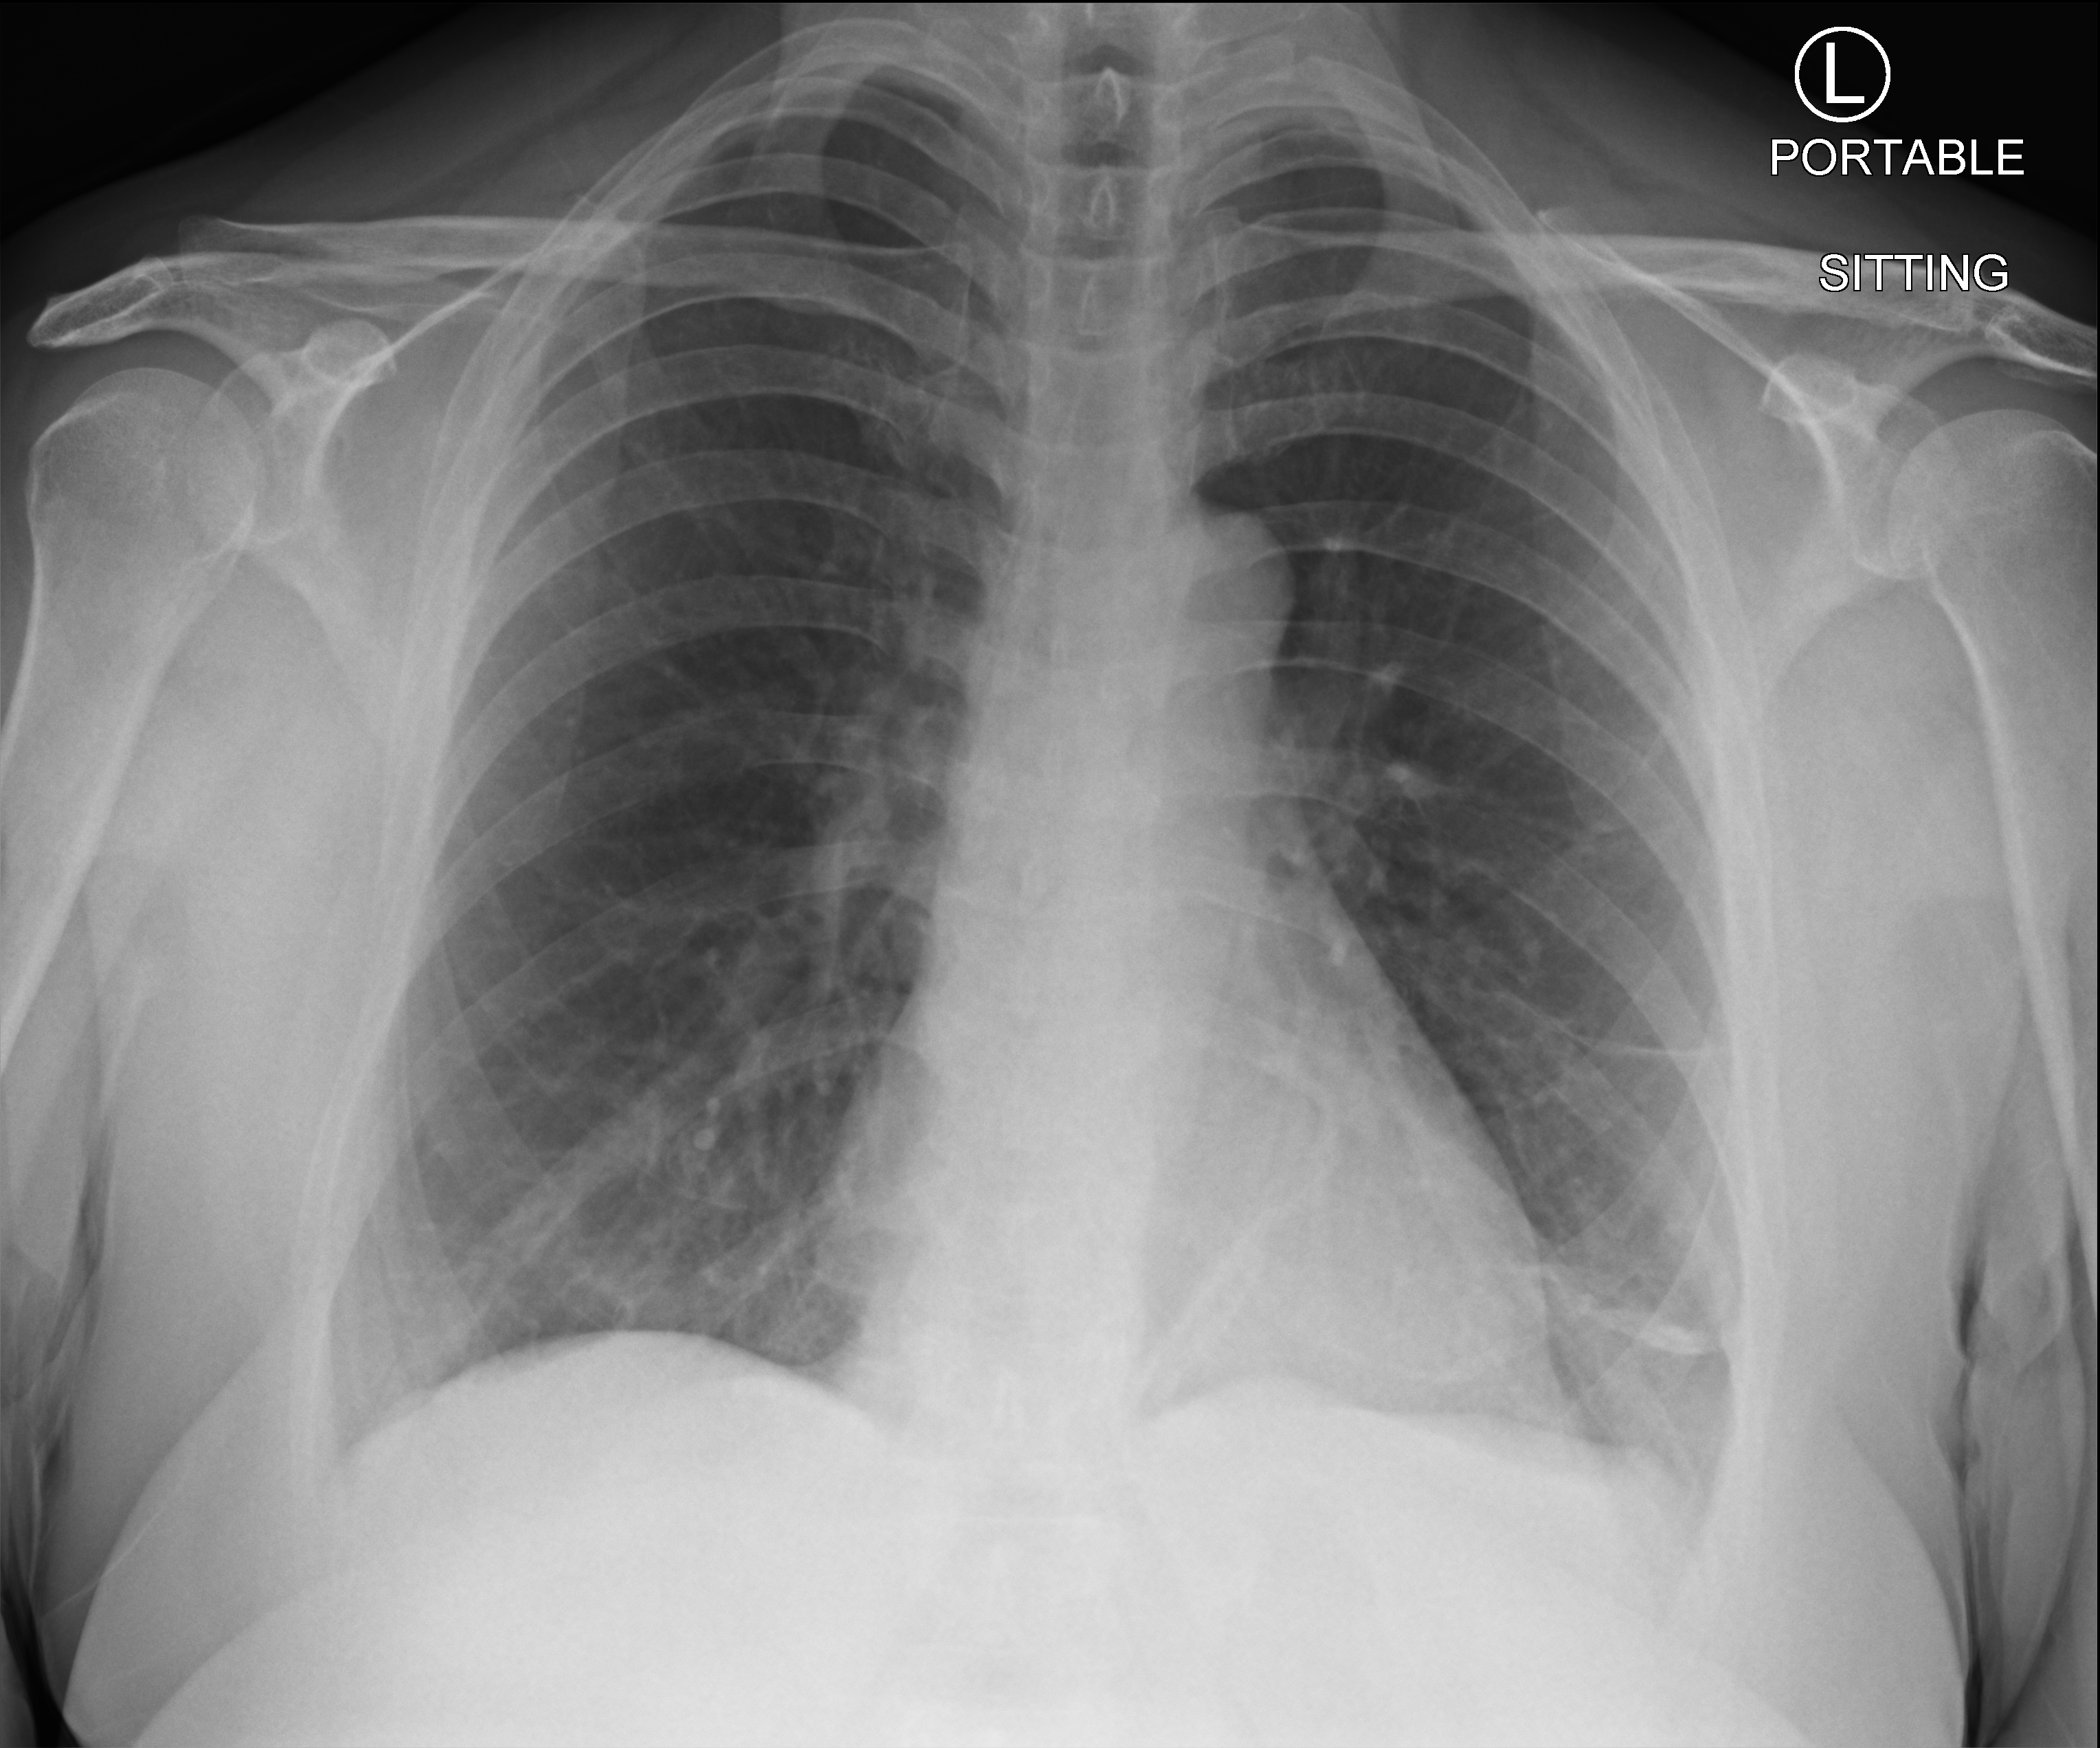
Chest X-ray (portable). Female patient hospitalised with COVID-19, age 18–59 years.
Hospital-stay facts (about this admission, not read from this image; timing relative to this image not recorded): mechanically ventilated during this hospital stay: no; length of hospital stay: 1 day; admitted to intensive care during this hospital stay: no.